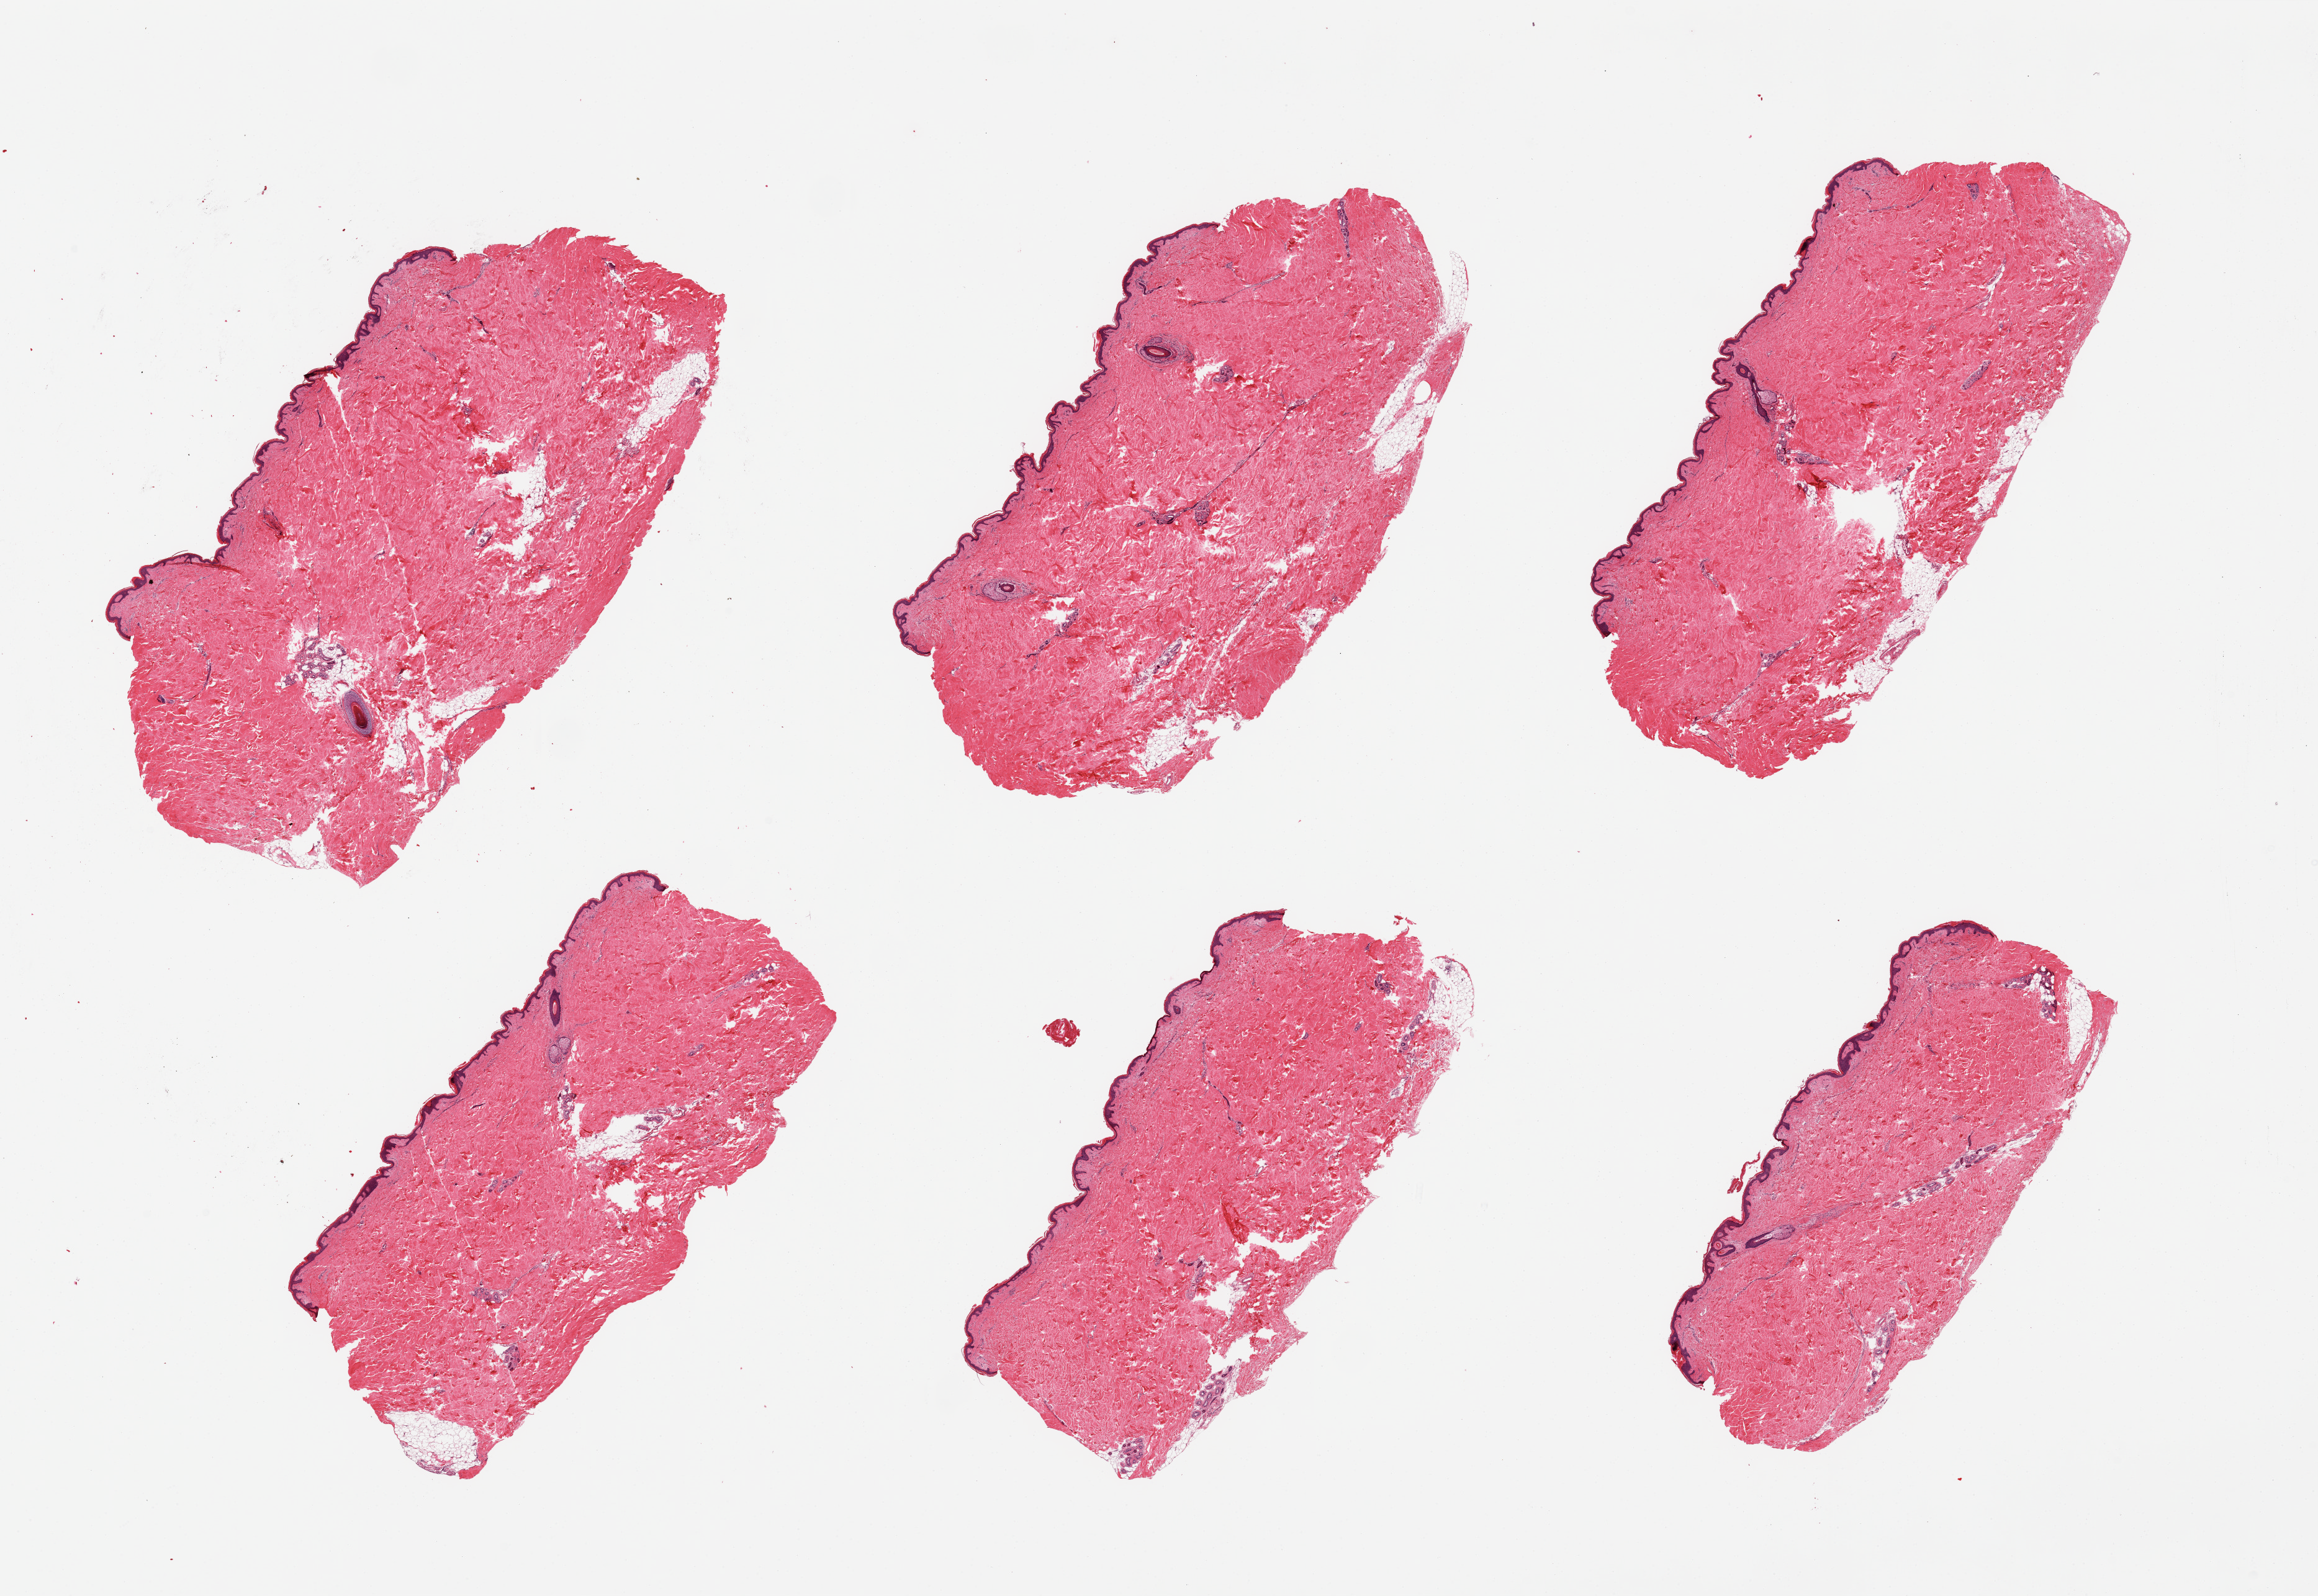
Digitized H&E-stained section — shown as a low-resolution overview of the whole scanned area (about 29.5 x 20.3 mm, acquisition: 20x scan); PAXgene-fixed, paraffin-embedded tissue; section of skin of suprapubic region (target tissue); tissue donor sample. Donor: male.
* reviewer comment on this tissue sample: 6 pieces; well trimmed, minimal internal fat